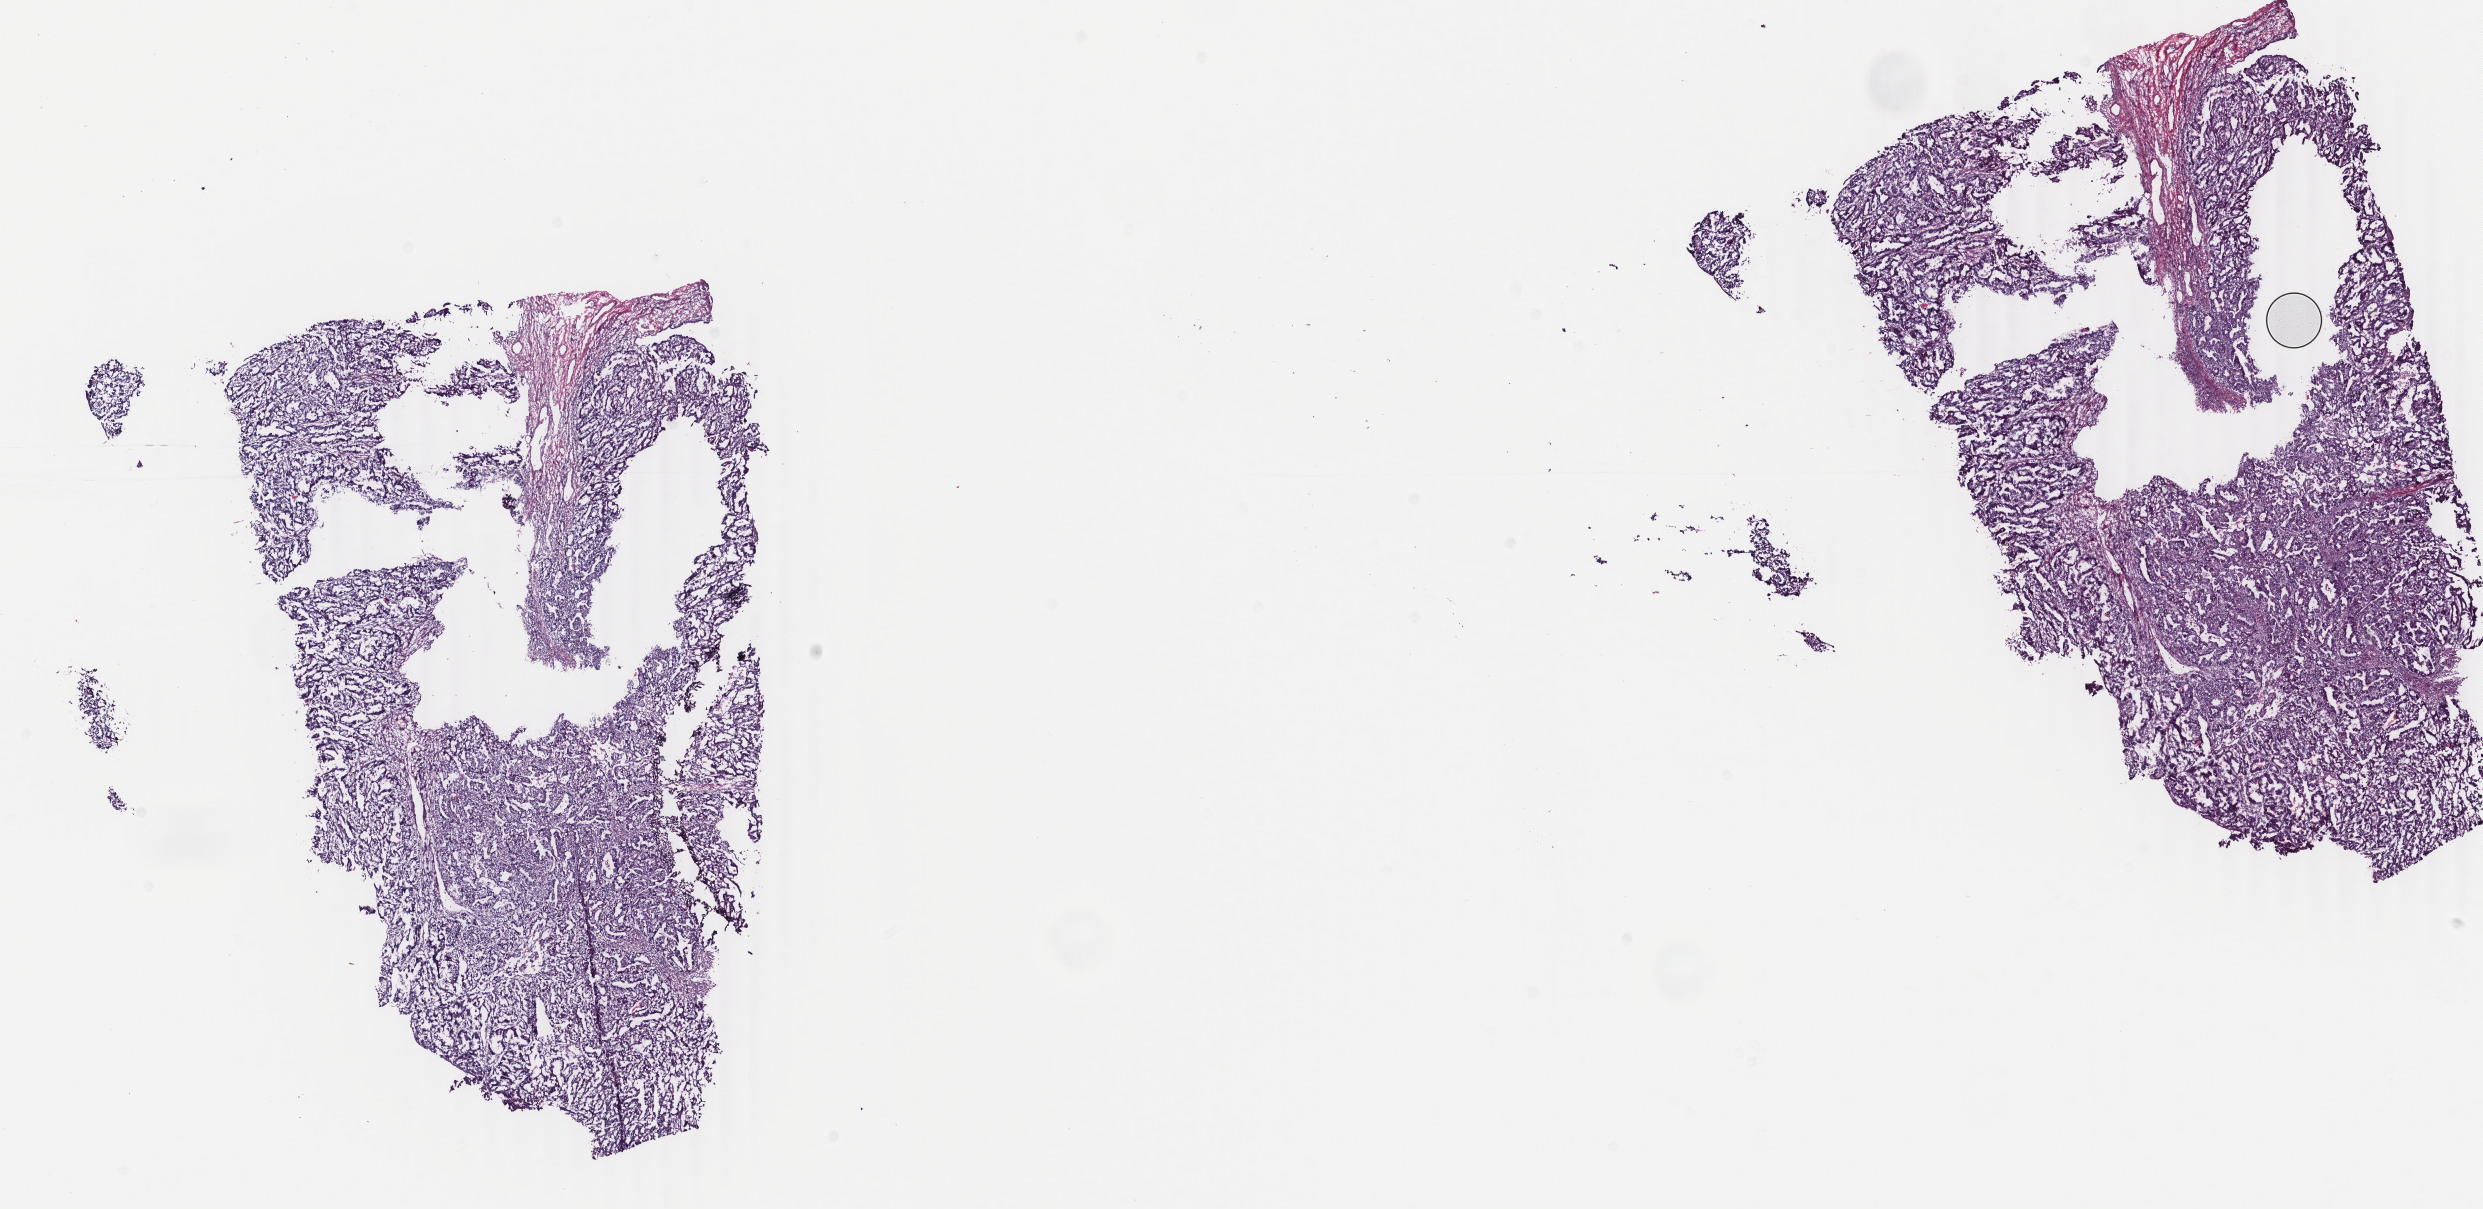
Digitized H&E tissue section (whole slide), low-resolution overview of the scanned area, about 19.8 x 9.6 mm. Frozen section from the top of the tissue portion. Uterus, primary tumour sample. Female, age 49 years at initial diagnosis. Histologic grade: G2 (moderately differentiated). Pathologist review of this section (percent, as recorded): tumour cells 95%, tumour nuclei 75%, normal cells 0%, stromal cells 5%, necrosis 0%. Infiltration values recorded for this section: lymphocyte infiltration 0%, monocyte infiltration 0%, neutrophil infiltration 0%.
FIGO stage: IB. Histologic diagnosis: Endometrioid adenocarcinoma, NOS (endometrium).